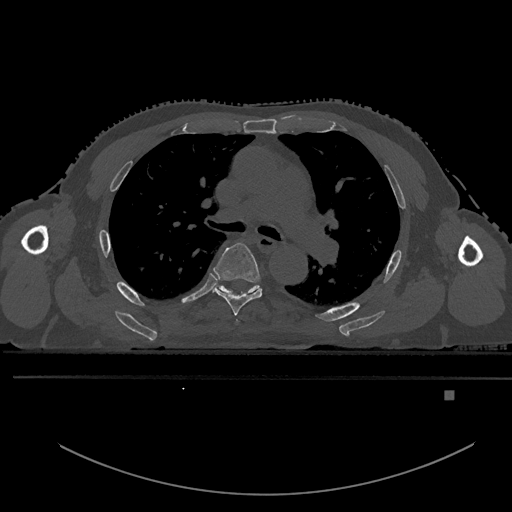
CT including the spine, one axial slice; position 349 of 969 along the scan axis; bone window (W 1800 / L 400 HU); 0.5 mm slice thickness; 512 × 512 image matrix, field of view 456 × 456 mm. Patient: male, 82 years. Case-level facts recorded for this patient, not image findings: primary cancer: prostate; vertebrae with lytic lesions (as recorded): T11, T9, T8, T2.
Structures marked on this image (semi-automatically segmented with operator editing):
- T4 vertebra: bounding box (x1, y1, x2, y2) in pixels: (236, 320, 239, 322)
- T5 vertebra: (213, 242, 263, 316)
- T6 vertebra: (212, 284, 260, 295)